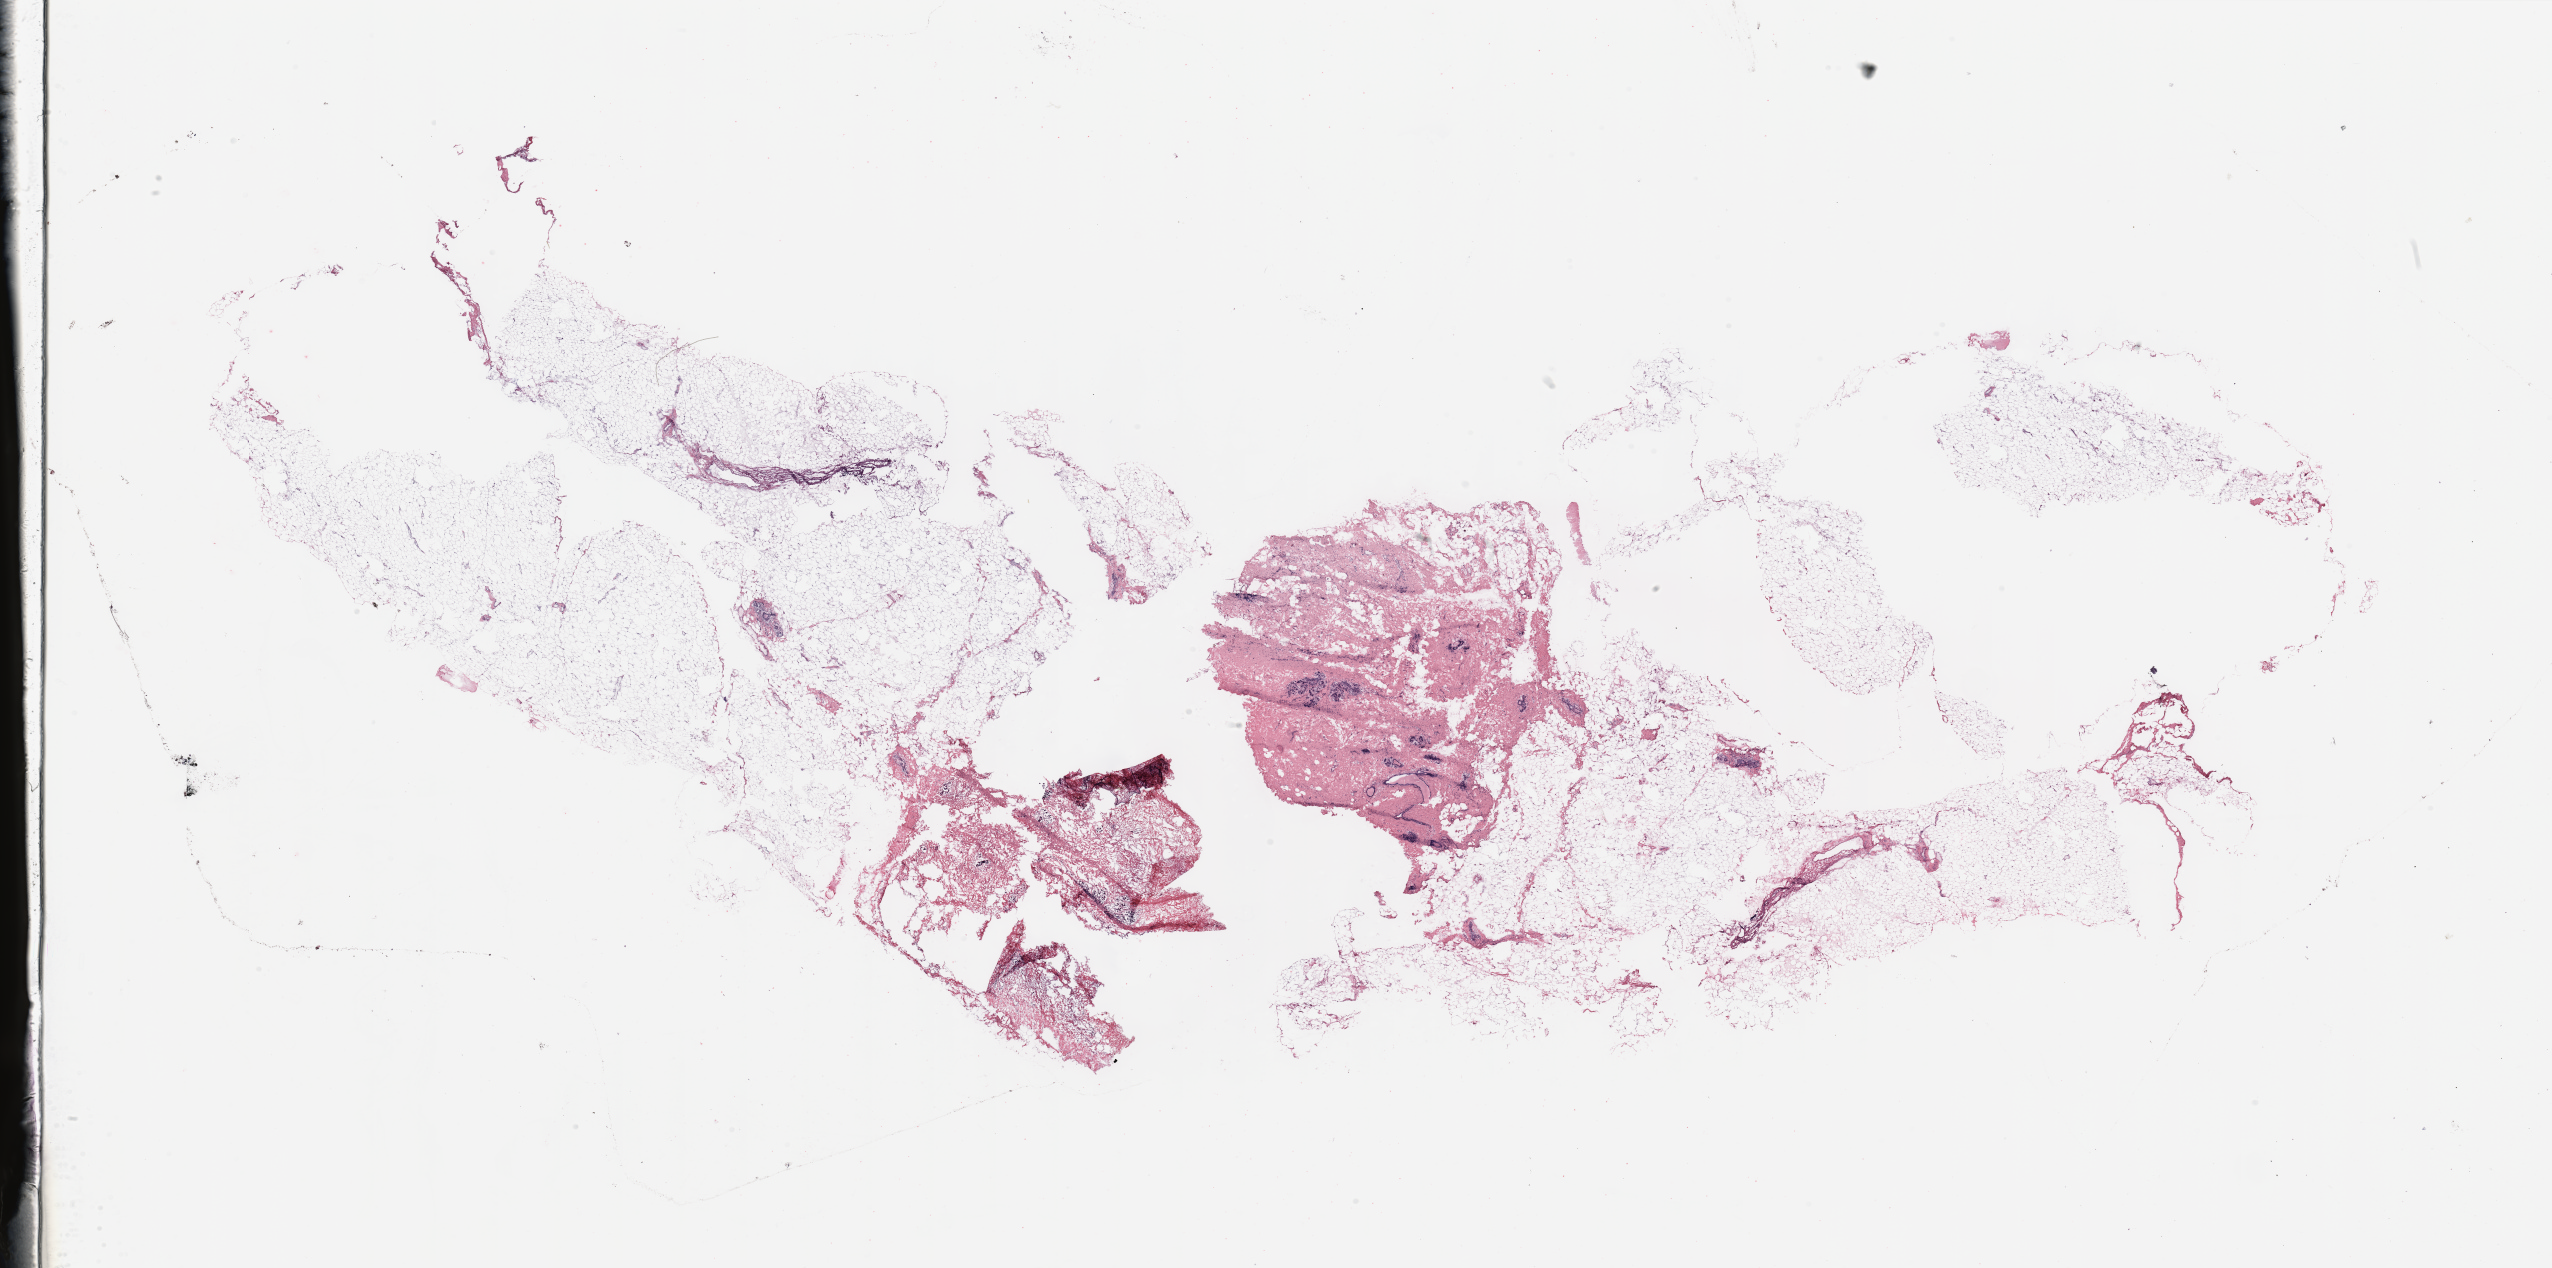
Whole-slide histology image, Hematoxylin and eosin (H&E) stained, whole scanned area (about 40.4 x 20.1 mm) shown as a low-resolution overview, breast, tumour tissue. Patient: female, age 50 years.
AJCC pathologic stage: IIA. Histologic diagnosis: Infiltrating duct carcinoma, NOS.